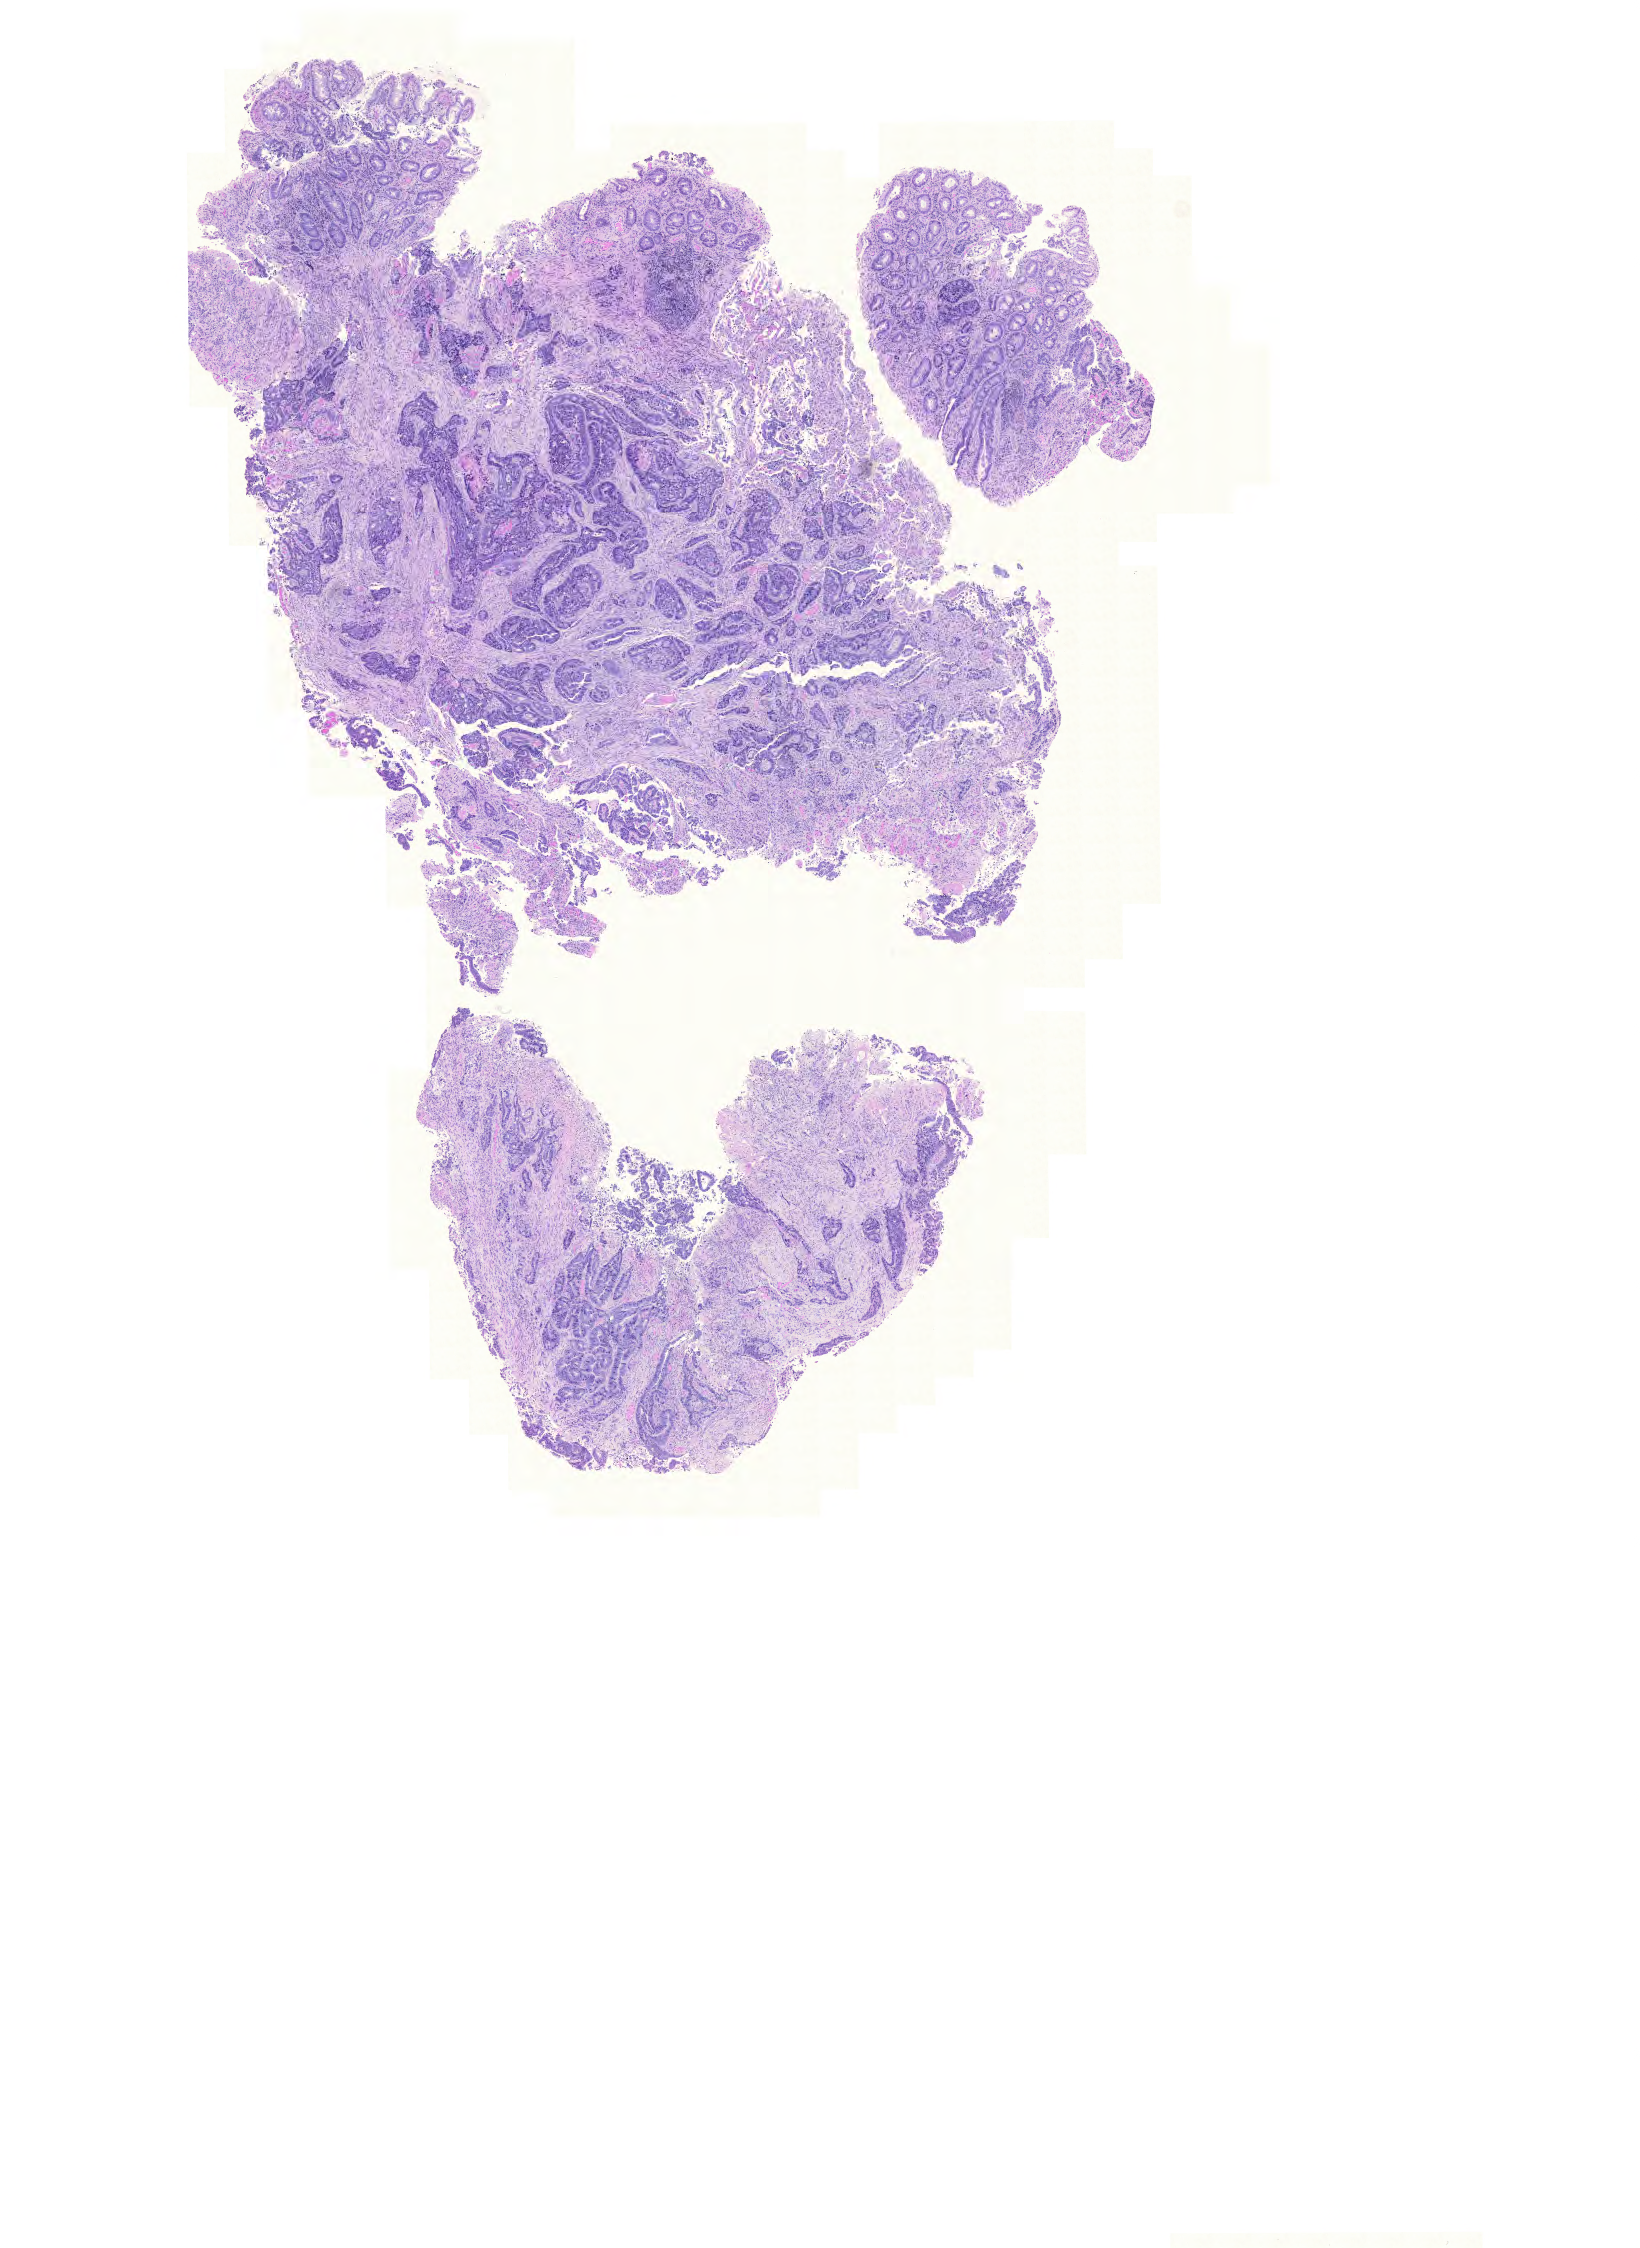
H&E whole-slide image — low-resolution overview of the scanned area, about 12.2 x 16.7 mm; FFPE section; primary tumour sample from the rectum. Male patient; age at initial diagnosis 63 years.
AJCC pathologic stage: IIA (6th edition). Lymph nodes positive (case pathology): 0 of 15 examined. Diagnosis: Adenocarcinoma, NOS (colon, NOS).